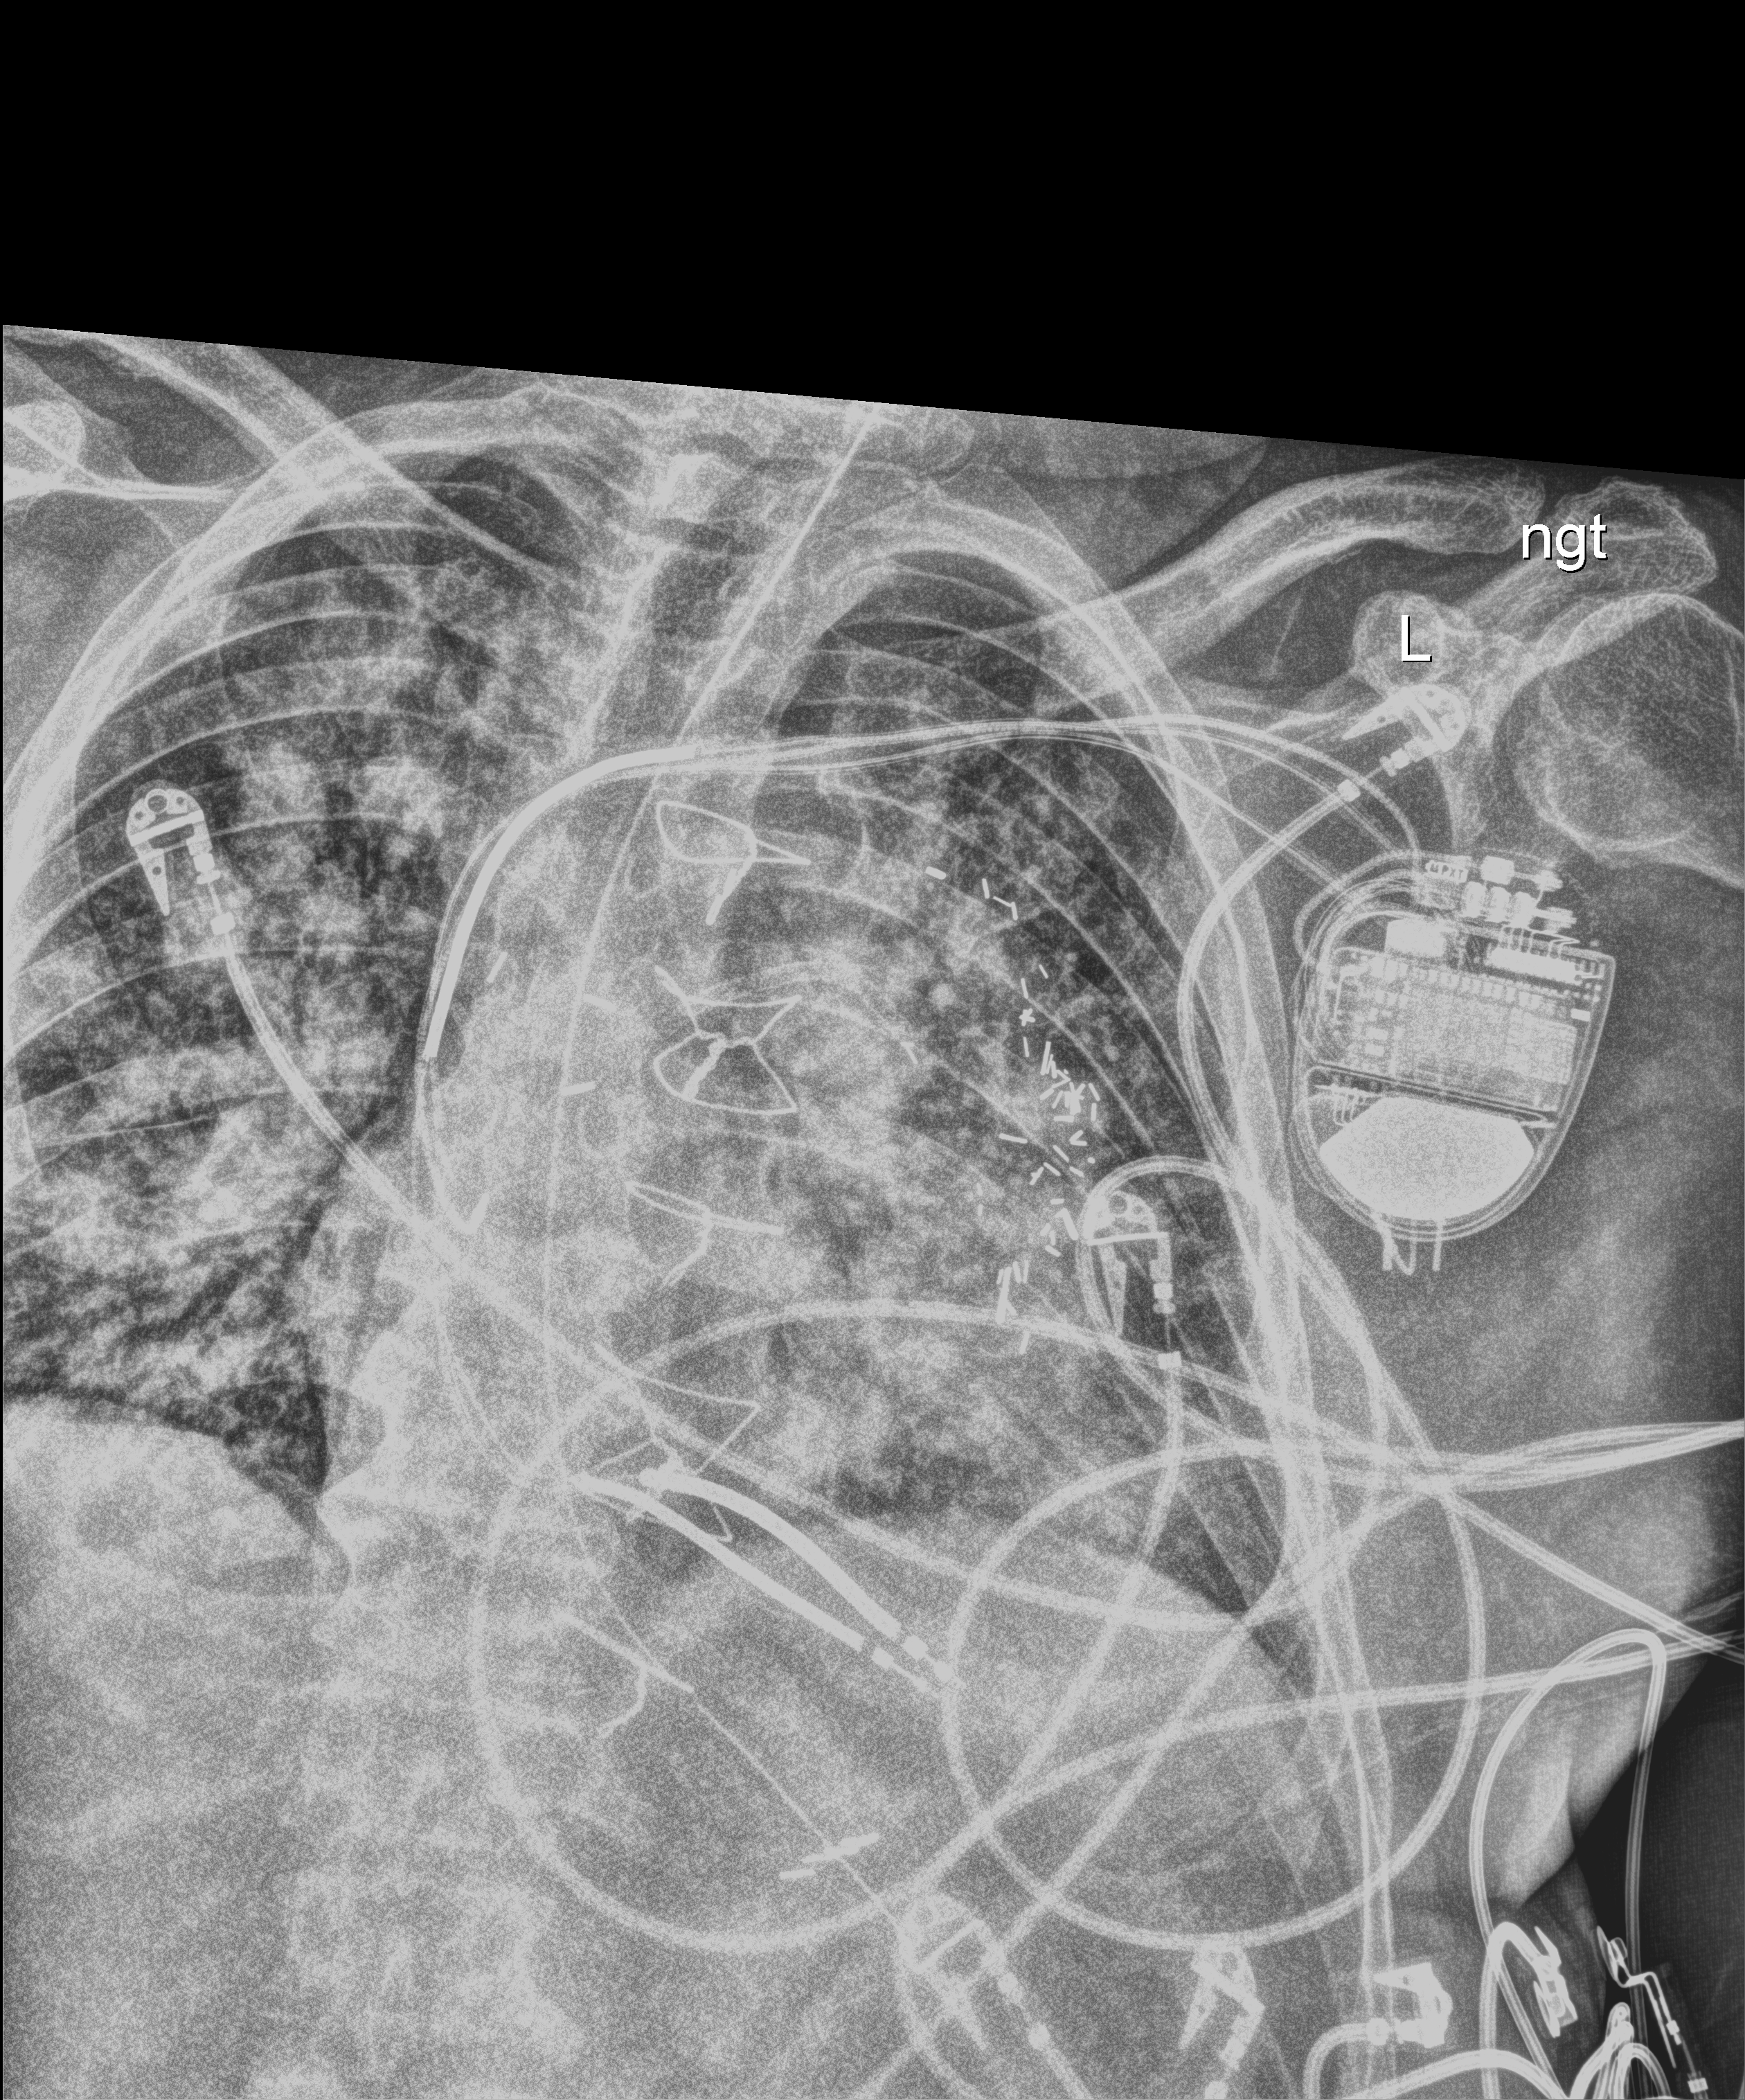
Chest X-ray (portable); anteroposterior (AP) projection. Male patient hospitalised with COVID-19, age 60–74 years.
From the hospital-stay record, not from the radiograph (when in the stay this image was taken is not recorded):
- other chronic lung disease (admission record): no